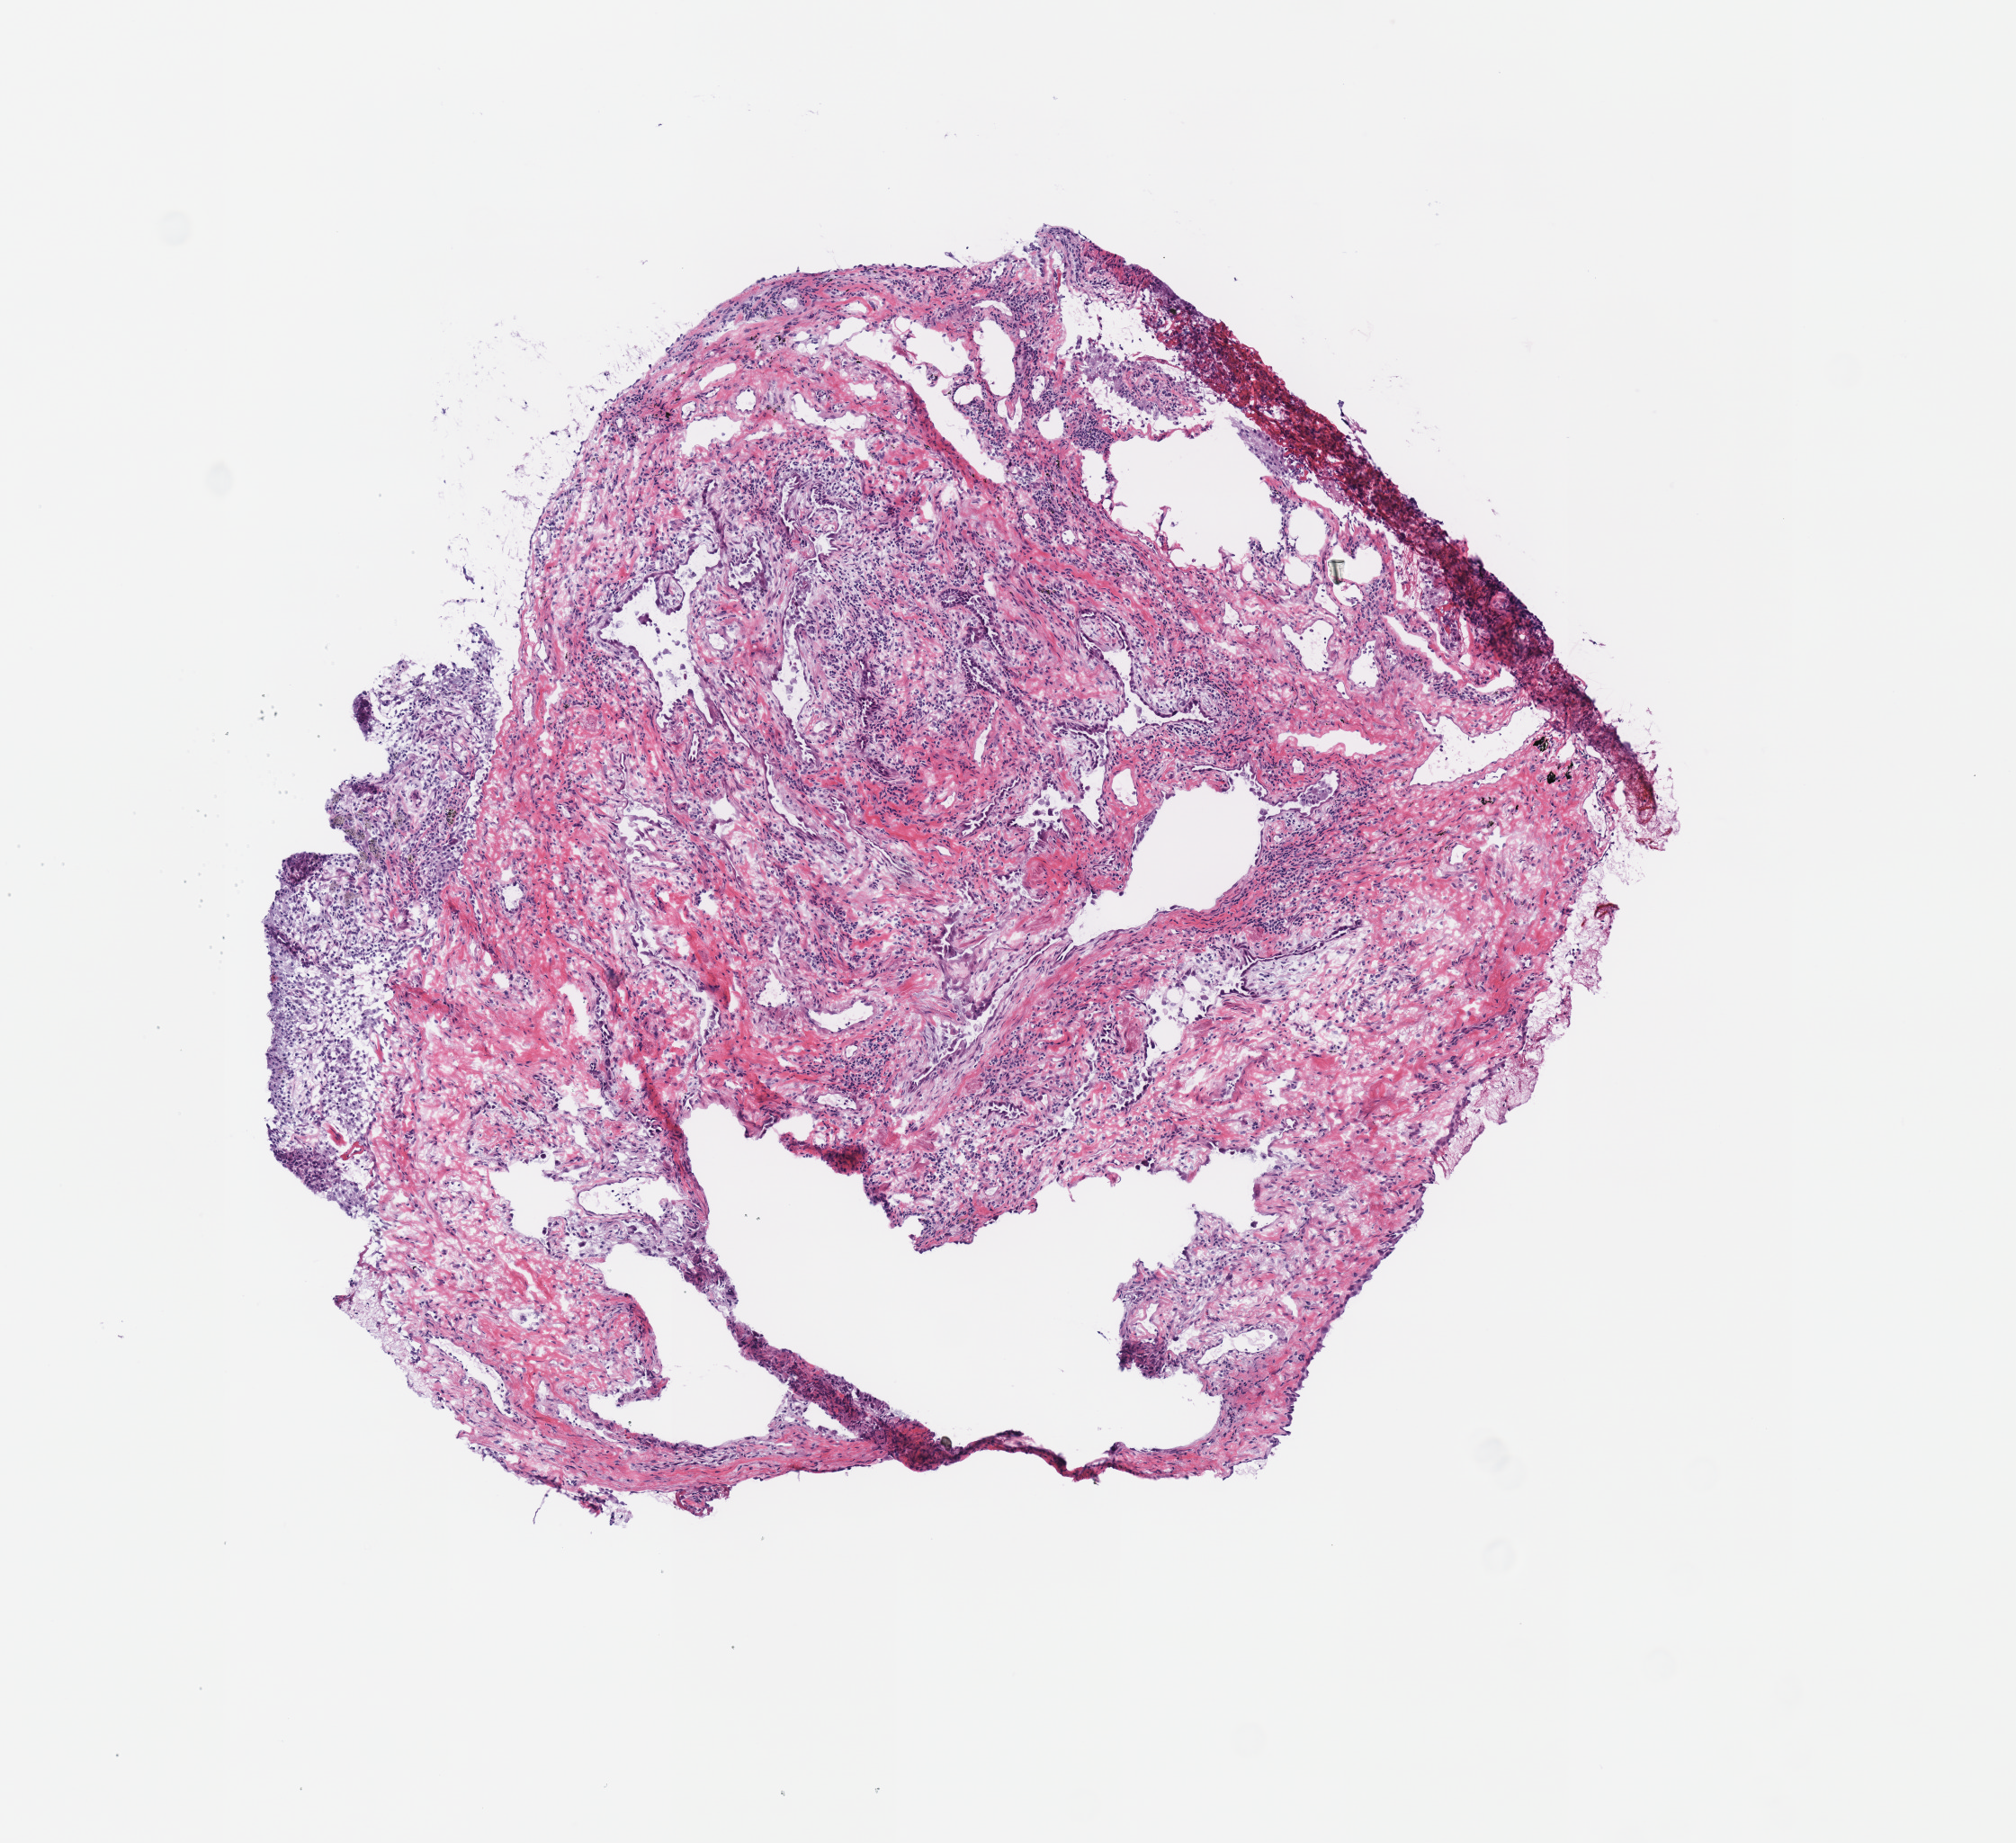
H&E whole-slide image, whole scanned area (about 4.4 x 4.0 mm) shown as a low-resolution overview; frozen section from the top of the tissue portion; solid tissue normal (non-tumour tissue) sample from the lung. Male patient; age at initial diagnosis 63 years.
This section: solid tissue normal (non-tumour) sample from the same patient. Patient diagnosis: Squamous cell carcinoma, NOS (lower lobe, lung).